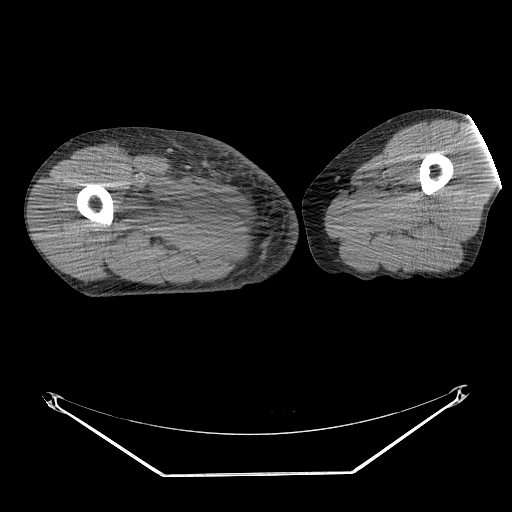
CT of an extremity soft-tissue mass (from a PET/CT study), one axial slice; position 240 of 311 along the scan axis; 140 kVp; soft-tissue window (W 400 / L 40 HU); 512 × 512 image matrix, field of view 500 × 500 mm. Male patient. From the clinical record (not read from this slice): histological type: undifferentiated - pleiomorphic; grade: high; site of the primary tumour: right thigh.
Annotated regions visible in this slice (expert contour drawn on MRI and transferred to this co-registered scan by the dataset authors):
- gross tumour volume including surrounding oedema: bounding box (x1, y1, x2, y2) in pixels: (130, 176, 211, 234)
- gross tumour volume (mass): (183, 201, 207, 218)